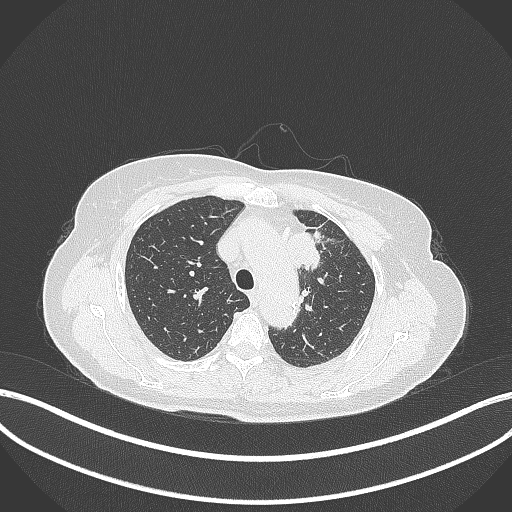
Chest CT, one axial slice; slice 250 of 369 in the series (ordered by position); 120 kVp; lung window (W 1500 / L -600 HU); 1 mm slice thickness; 512 × 512 image matrix, field of view 400 × 400 mm. Female patient, age 65 years. From the clinical record (not read from this slice): clinical TNM (as recorded): T2a N0 M0.
Structures marked on this image (bounding box drawn by a radiologist):
- lung tumour (recorded histology: adenocarcinoma): bounding box [x1, y1, x2, y2] px = [283, 227, 328, 273]